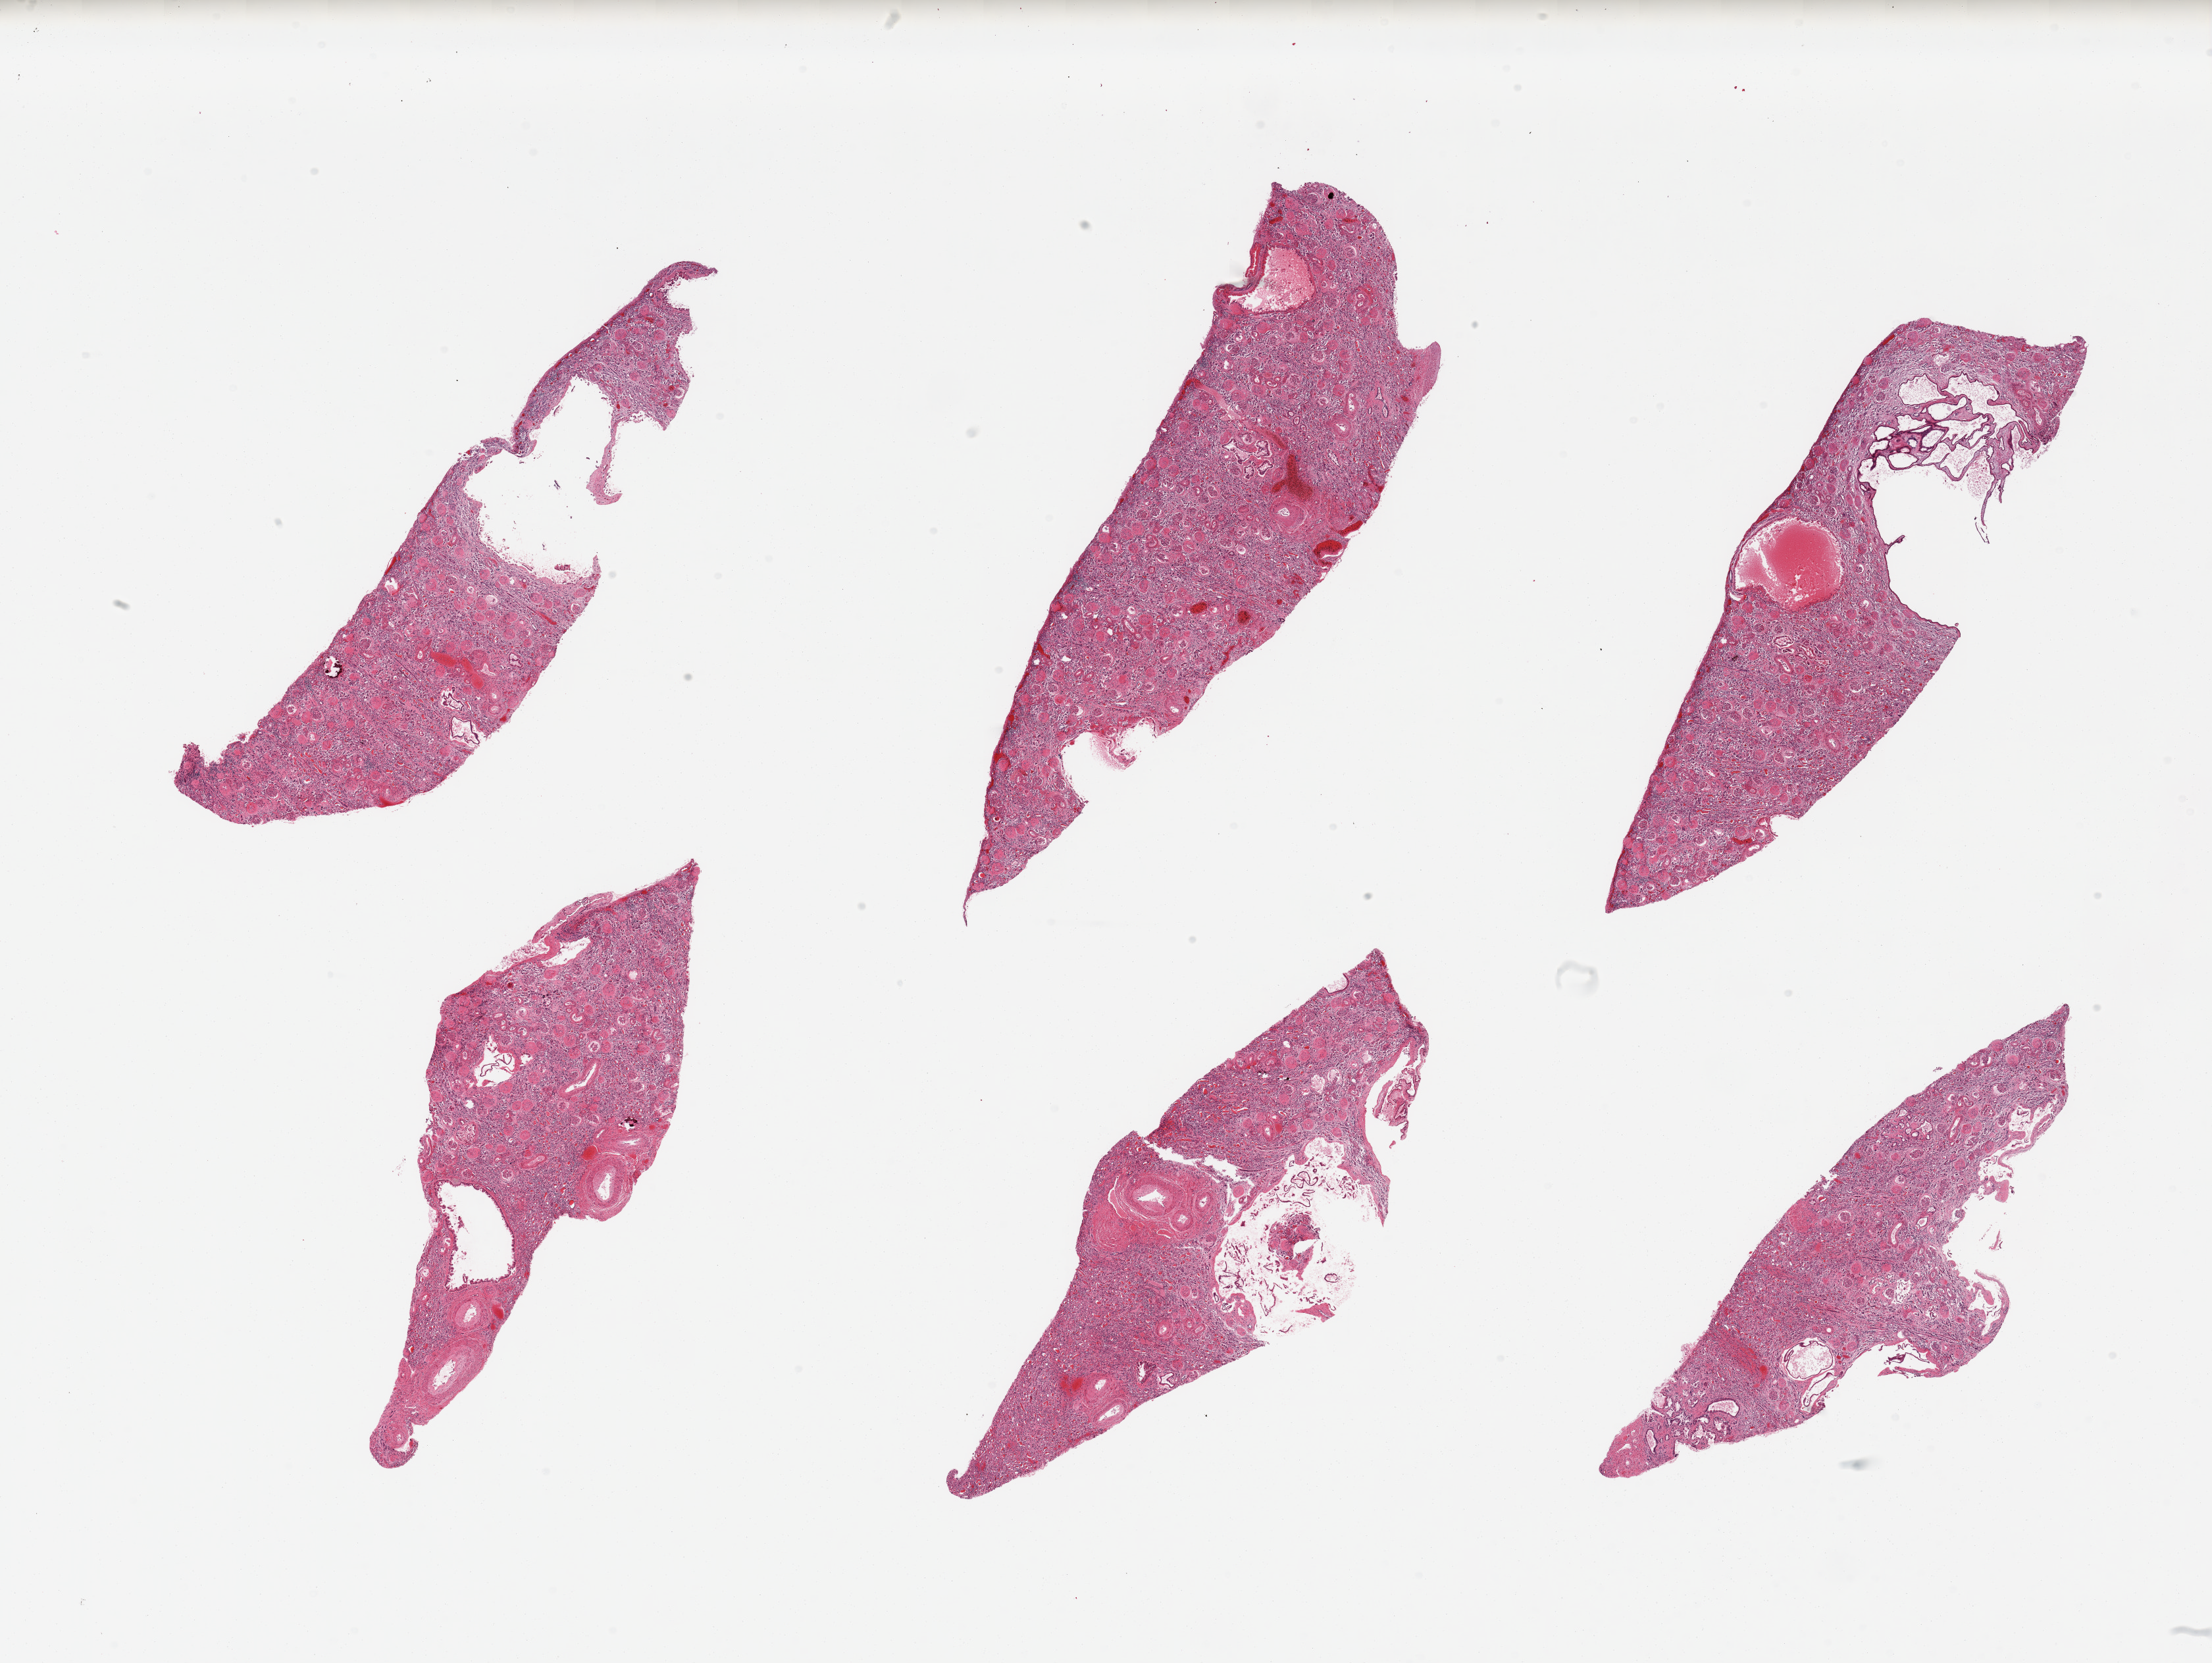
Haematoxylin and eosin whole-slide image, brightfield — low-resolution overview of the scanned area, about 26.6 x 20.0 mm. PAXgene-fixed paraffin-embedded (PFPE) section. Section of renal cortex (target tissue). Tissue donor sample. Donor: male.
Pathologist's review note for this sample: 6 pieces; numerous variably sized simple cysts; renal cortex with severe arterio and arteriolonephrosclerosis and ~90% hyalinized glomeruli; focal tubular calcifications.